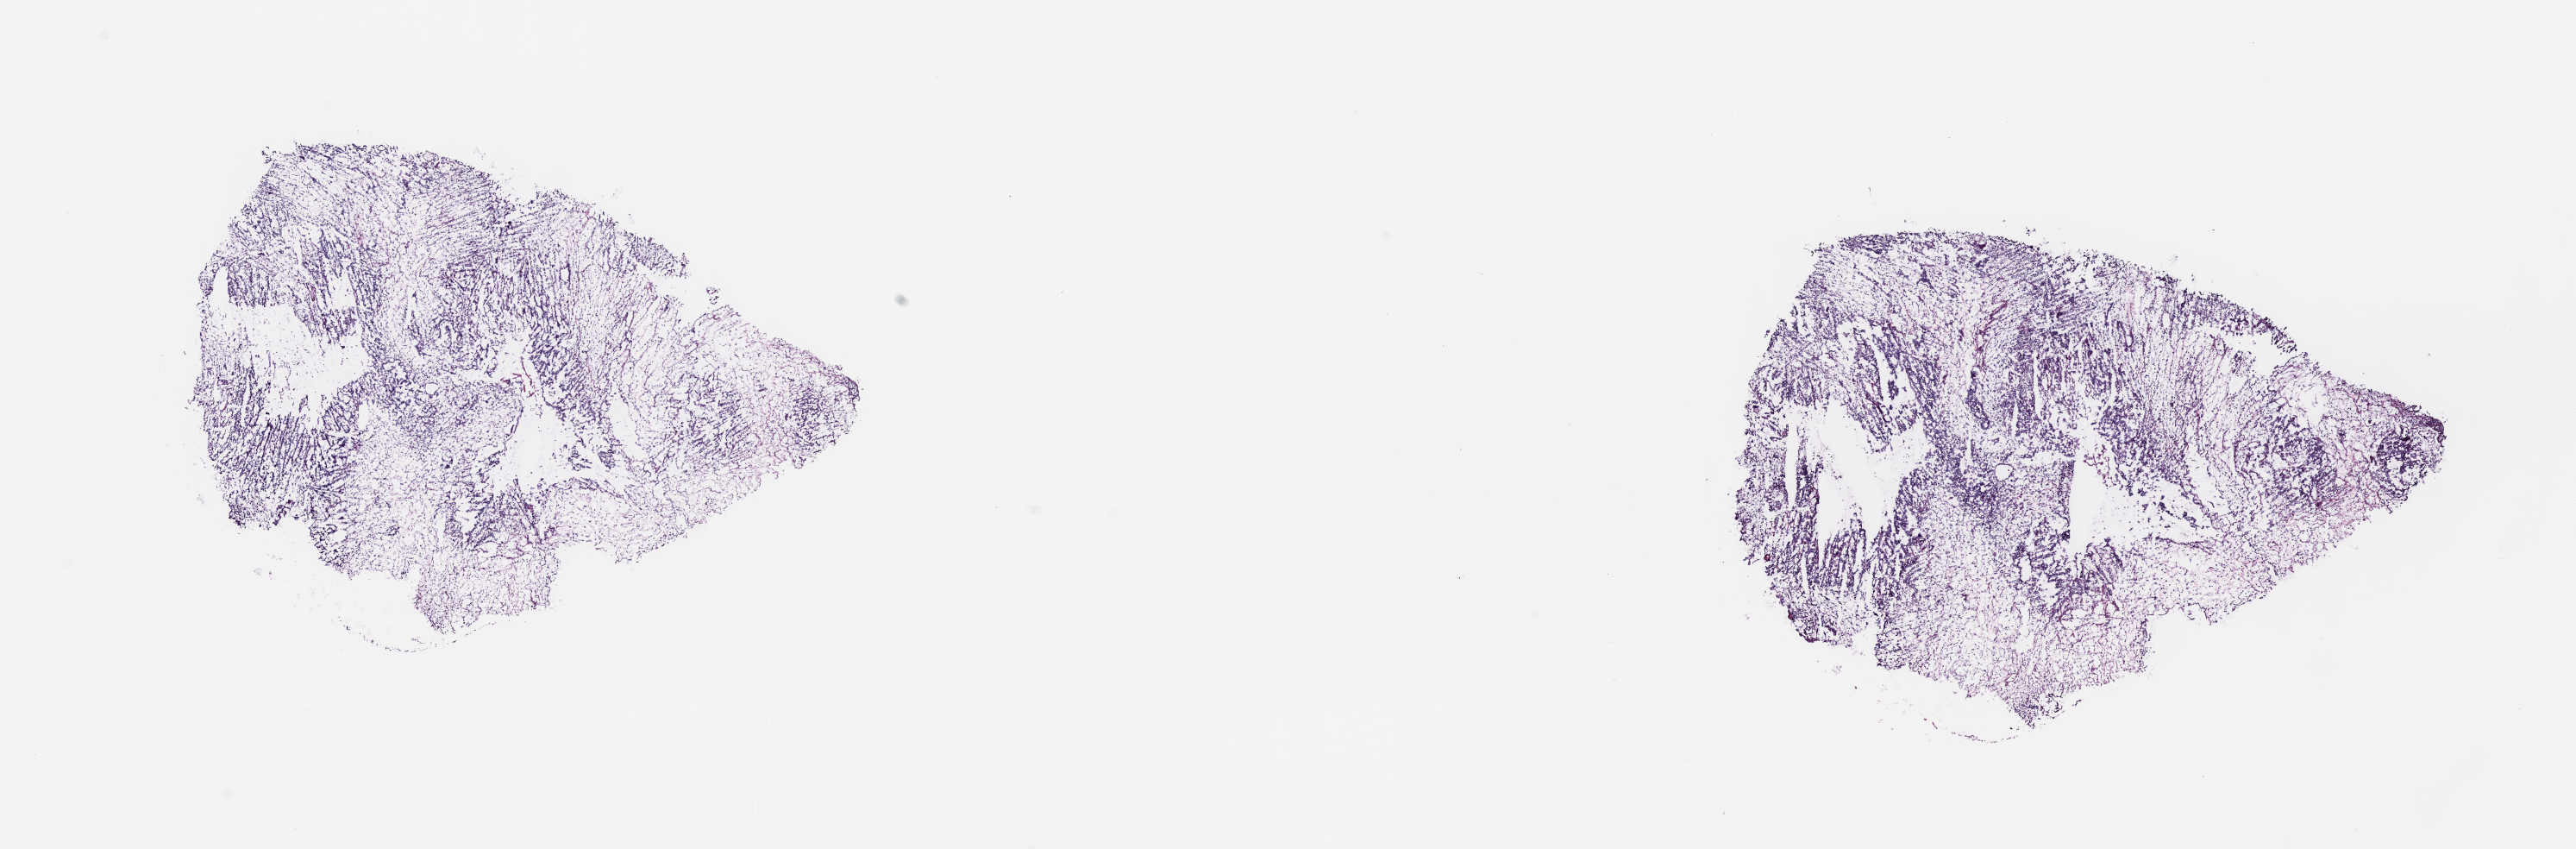
Whole-slide histology image, H&E, low-resolution overview of the scanned area, about 24.2 x 8.0 mm, frozen section from the top of the tissue portion, primary tumour sample from the testis. Male patient; age at initial diagnosis 33 years. Pathologist review of this section (percent, as recorded): tumour cells 100%, tumour nuclei 65%, normal cells 0%, stromal cells 0%, necrosis 0%. Inflammatory infiltration, as recorded: lymphocyte infiltration 0%, monocyte infiltration 0%, neutrophil infiltration 0%.
AJCC pathologic stage: IS (7th edition). Diagnosis: Mixed germ cell tumor. Laterality: left.